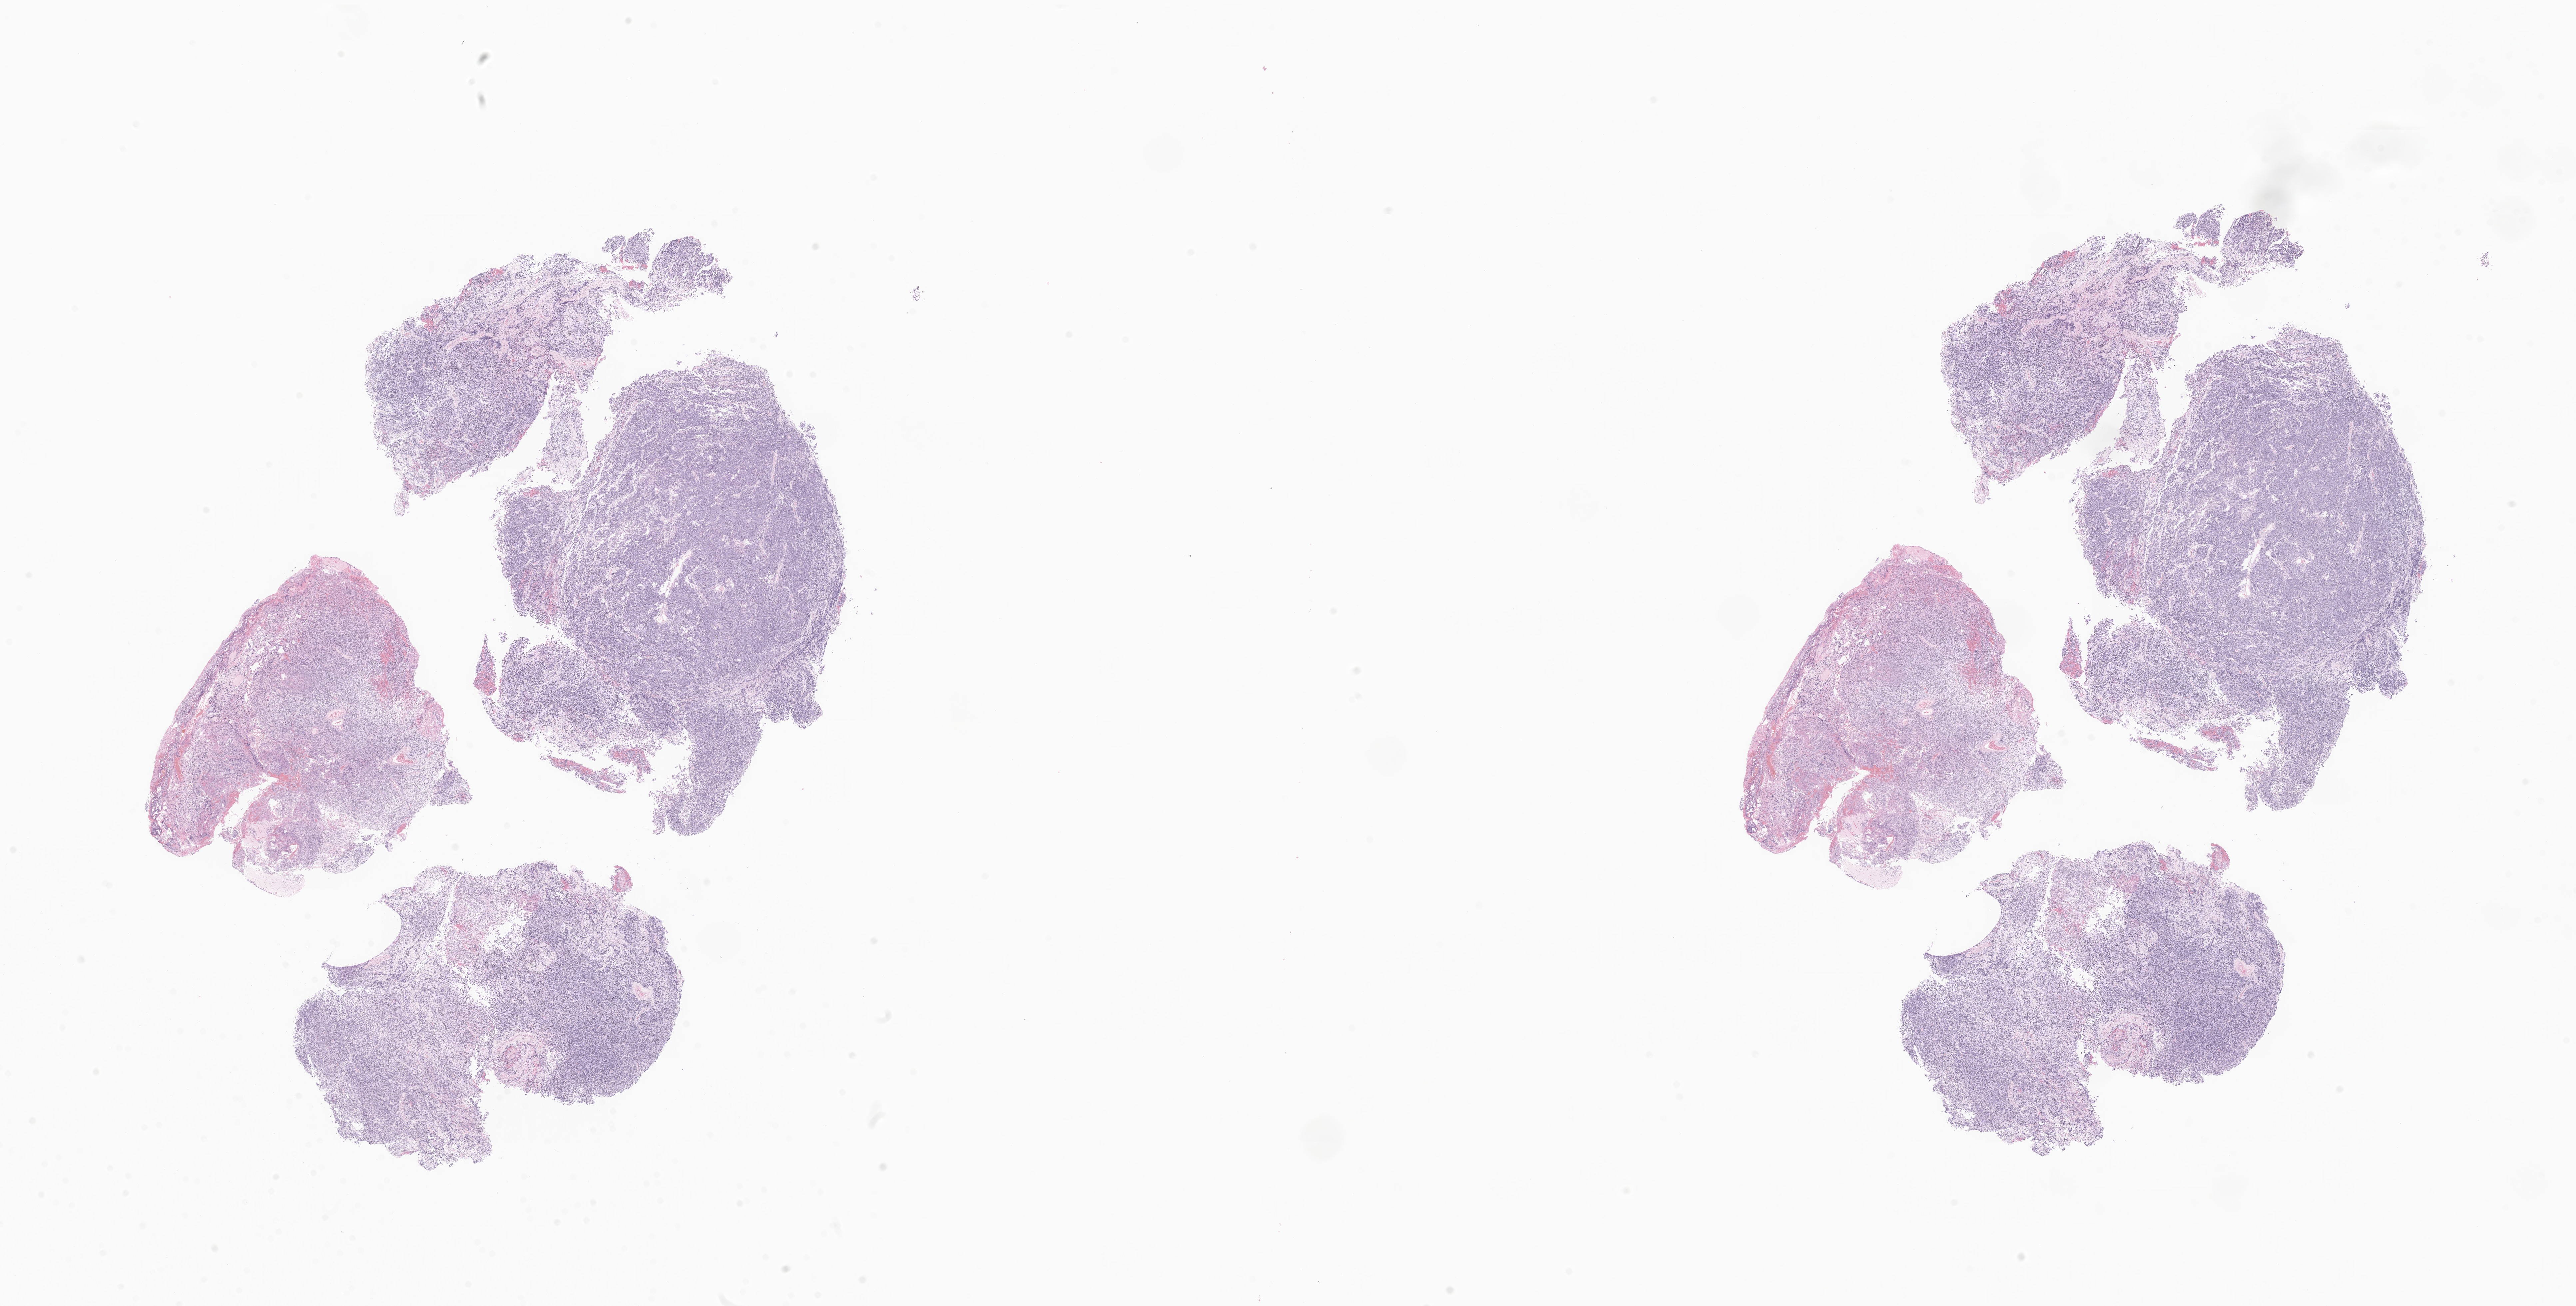
Whole-slide image, H&E stain of tumor tissue from the cerebellum — shown as a low-resolution overview of the whole scanned area (about 32.6 x 16.5 mm). Formalin-fixed paraffin-embedded section. Patient male; age 44 months (3 years 8 months).
Diagnosis: Large cell medulloblastoma.